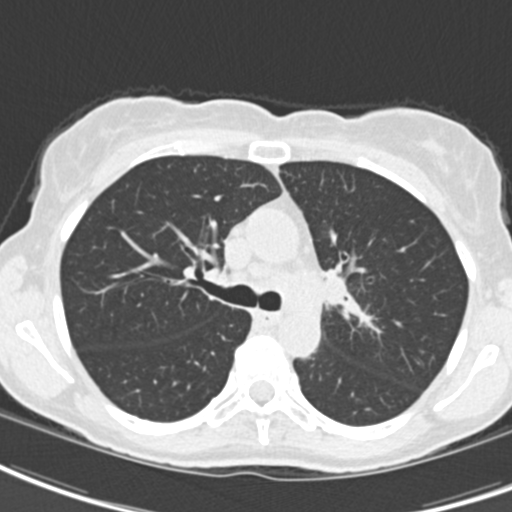
Chest CT (low-dose screening protocol), one axial image. First (baseline) screen. Lung window (W 1500 / L -600 HU). 2 mm slice thickness. Female, age 62 years at enrolment. Current smoker at enrolment.
Expert reader's lesion annotation, box from (x=293, y=252) to (x=366, y=336) px. Screening reader's record for this exam (one nodule recorded; not confirmed to be the boxed lesion): non-calcified nodule or mass ≥4 mm, right upper lobe, 24 × 20 mm, smooth margins, ground glass attenuation. Note: the box lies in the patient's left hemithorax on this image, whereas the reader's record names the right lung; they may be different findings. Official screen result: positive, change unspecified: nodule(s) >= 4 mm or enlarging nodule(s), mass(es), or other non-specific abnormalities suspicious for lung cancer. Participant outcome: lung cancer diagnosed 24 days after this screen — oat cell carcinoma, left hilum, left main stem bronchus, stage IIIB (AJCC 6th edition), 50 mm at pathology.